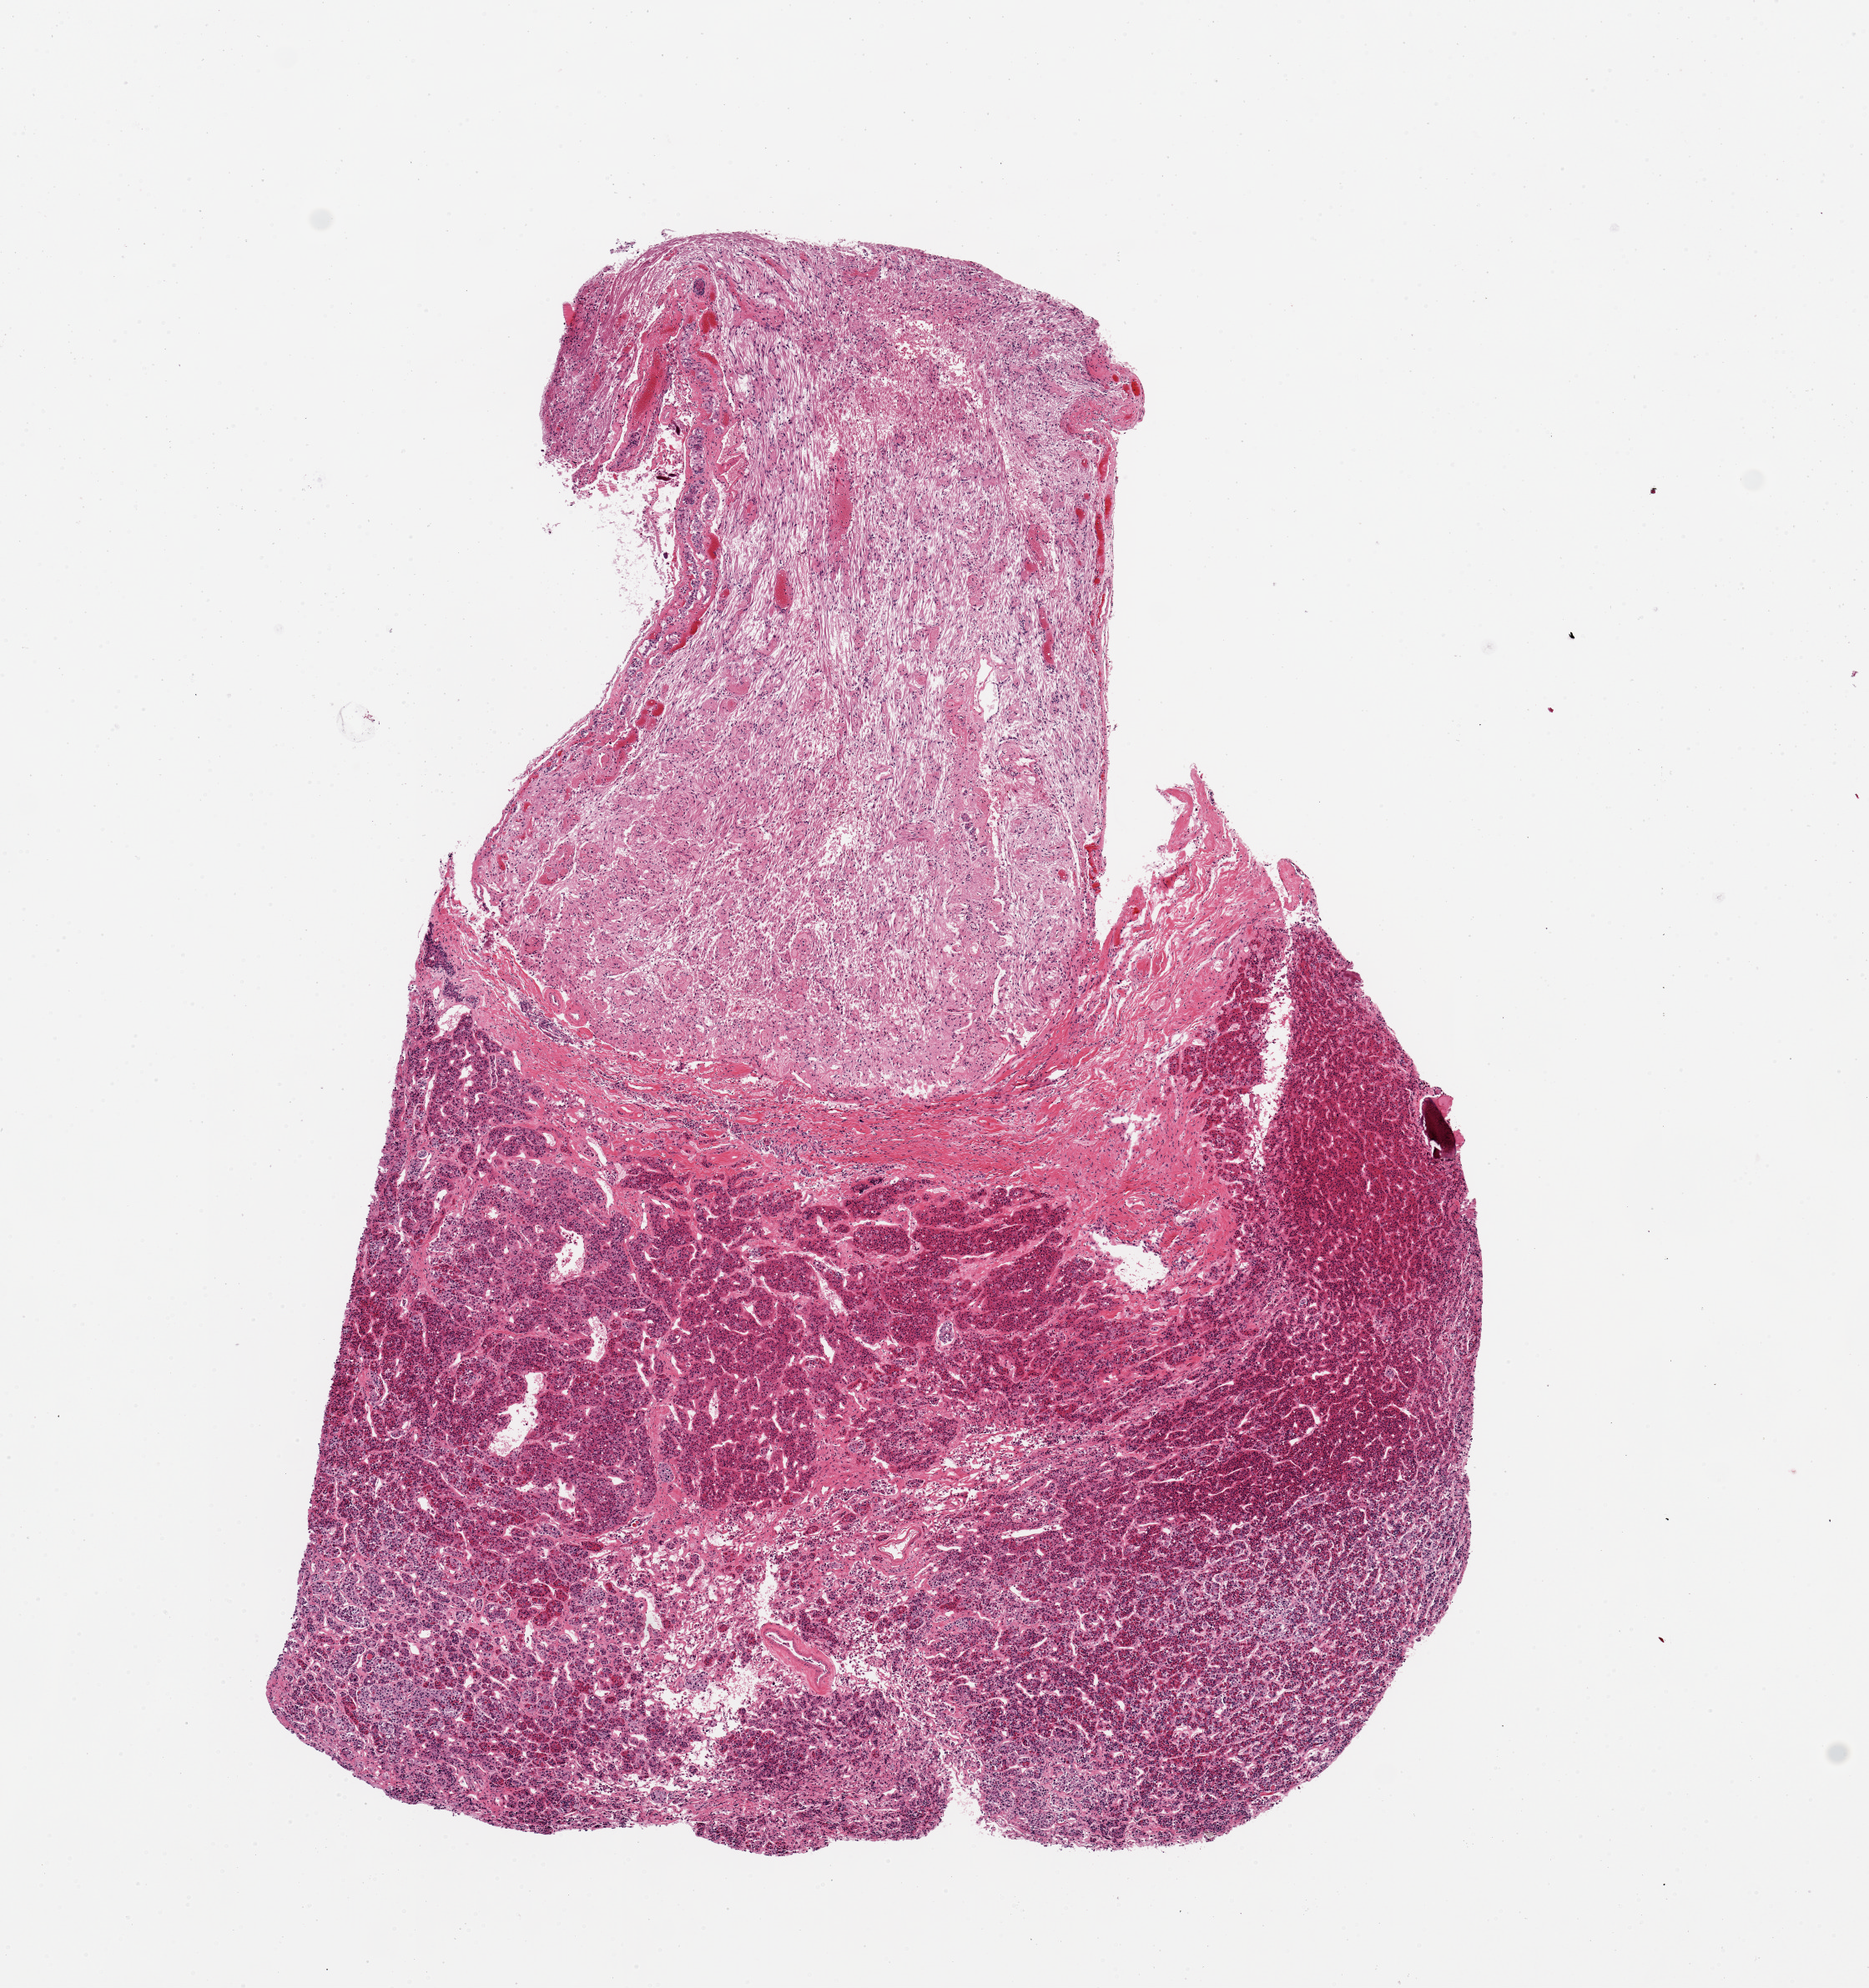
Whole-slide image, haematoxylin and eosin stain, brightfield — shown as a low-resolution overview of the whole scanned area (about 8.9 x 9.4 mm, acquisition: 20x scan). PAXgene-fixed, paraffin-embedded tissue. Sampled site (target tissue): pituitary. Donor tissue sample. Male donor.
- pathologist's review note for this sample: 1 piece; 8x6mm; ~50% neurohypophysis